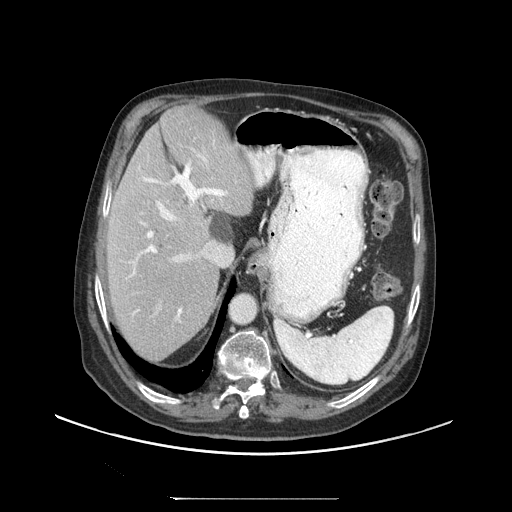
Contrast-enhanced abdominal CT (liver protocol), one axial slice. Position 71 of 97 along the scan axis. Reconstruction kernel STANDARD. Soft-tissue window (W 400 / L 40 HU). 2.5 mm slice thickness. 512 × 512 image matrix, field of view 450 × 450 mm. Case-level facts recorded for this patient, not image findings: diagnosis: hepatocellular carcinoma (patient treated with transarterial chemoembolisation; whether this scan precedes or follows treatment is not stated here); TNM stage (as recorded): Stage-IIIC; Child-Pugh class: A; tumour differentiation: well differentiated; tumour nodularity: uninodular.
Outlined on this slice (semi-automatically segmented with operator editing):
- abdominal aorta: bounding box [x1, y1, x2, y2] px = [230, 295, 256, 323]
- liver parenchyma outside the tumour (the mass and vessels are separate outlines, so this box may not span the whole liver): [106, 106, 256, 360]
- liver vessels: [130, 150, 231, 321]